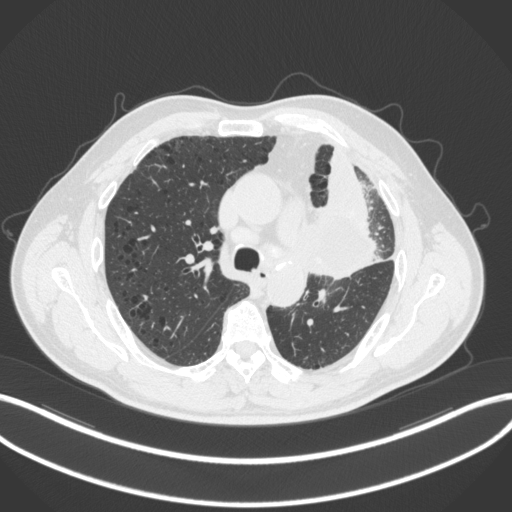
Chest CT, one axial slice; slice 193 of 286 in the series (ordered by position); 120 kVp; lung window (W 1500 / L -600 HU); 512 × 512 image matrix. Patient: male, 68 years. From the clinical record (not read from this slice): clinical TNM (as recorded): T3 N3 M1.
Annotated regions visible in this slice (bounding box drawn by a radiologist):
- lung tumour (recorded histology: adenocarcinoma): bounding box (x1, y1, x2, y2) in pixels: (297, 196, 384, 279)